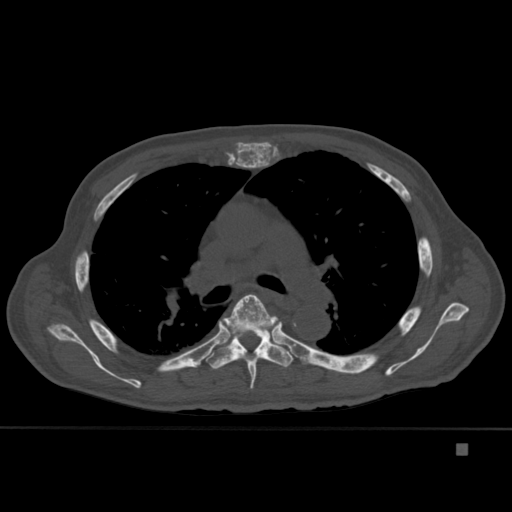
CT including the spine, one axial slice. Position 300 of 451 along the scan axis. Bone window (W 1800 / L 400 HU). 1.5 mm slice thickness. 512 × 512 image matrix, field of view 378 × 378 mm. Patient: male, 75 years. Case-level facts recorded for this patient, not image findings: primary cancer: prostate.
Outlined on this slice (semi-automatic segmentation, software-assisted and operator-edited):
- T5 vertebra: bounding box [x1, y1, x2, y2] px = [219, 294, 281, 389]
- T6 vertebra: [205, 322, 294, 369]